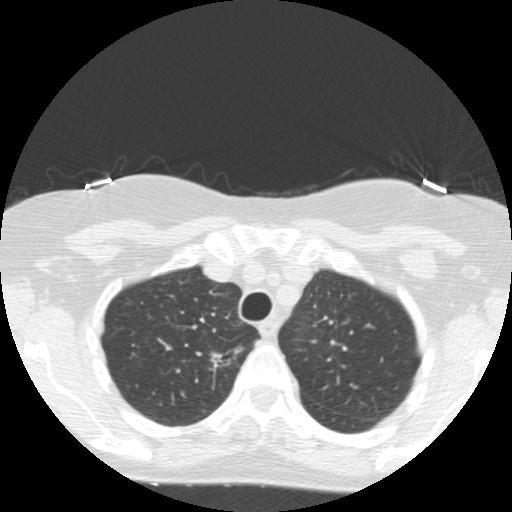
Axial slice from a low-dose chest CT screening exam; baseline screening round; lung window (W 1500 / L -600 HU); 2.5 mm slice thickness; standard (soft-tissue) reconstruction kernel (STANDARD); 512 × 512 image matrix, field of view 300 × 300 mm. Female participant, aged 67 years at enrolment. Former smoker at enrolment.
Lesion marked by an expert reader, bounding box [x1, y1, x2, y2] px = [195, 340, 255, 386]. Screening reader's record for this exam (one nodule recorded; not confirmed to be the boxed lesion): non-calcified nodule or mass ≥4 mm, right upper lobe, 16 × 7 mm, poorly defined margins, mixed attenuation. Official screen result: positive, change unspecified: nodule(s) >= 4 mm or enlarging nodule(s), mass(es), or other non-specific abnormalities suspicious for lung cancer. Lung cancer was diagnosed 132 days after this screen: adenocarcinoma, NOS, right upper lobe, moderately differentiated (G2), stage IA (AJCC 6th edition), 13 mm at pathology.